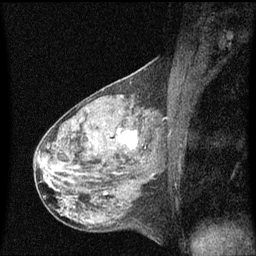
Breast MRI (dynamic contrast-enhanced), one sagittal slice; position 34 of 60 along the scan axis; dynamic contrast-enhanced series, image 2 of 3 at this slice position (ordered by acquisition); 1.5 T; TE 4.2 ms, TR 8 ms; 2 mm slice thickness; 256 × 256 image matrix, field of view 200 × 200 mm. Patient: female, 50 years.
Annotated regions visible in this slice (semi-automatic segmentation, software-assisted and operator-edited):
- analysis volume of interest (the breast-tissue region the enhancement analysis was run in; not a lesion): box from (x=106, y=118) to (x=148, y=159) px
- tumour enhancement mask (voxels above the 70 % enhancement threshold inside the analysis volume of interest): (x=117, y=130)–(x=138, y=149)